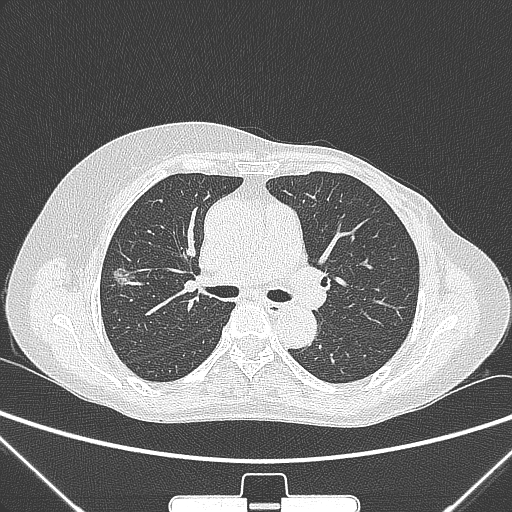
Chest CT, one axial slice. 120 kVp. Lung window (W 1500 / L -600 HU). 1 mm slice thickness. 512 × 512 image matrix, field of view 350 × 350 mm. Patient: female, 64 years. From the clinical record (not read from this slice): clinical TNM (as recorded): T1c N0 M0.
Annotated regions visible in this slice (rectangle marked by the reading radiologist):
- lung tumour (recorded histology: adenocarcinoma): bounding box <108,259,145,294> (left, top, right, bottom; pixels)